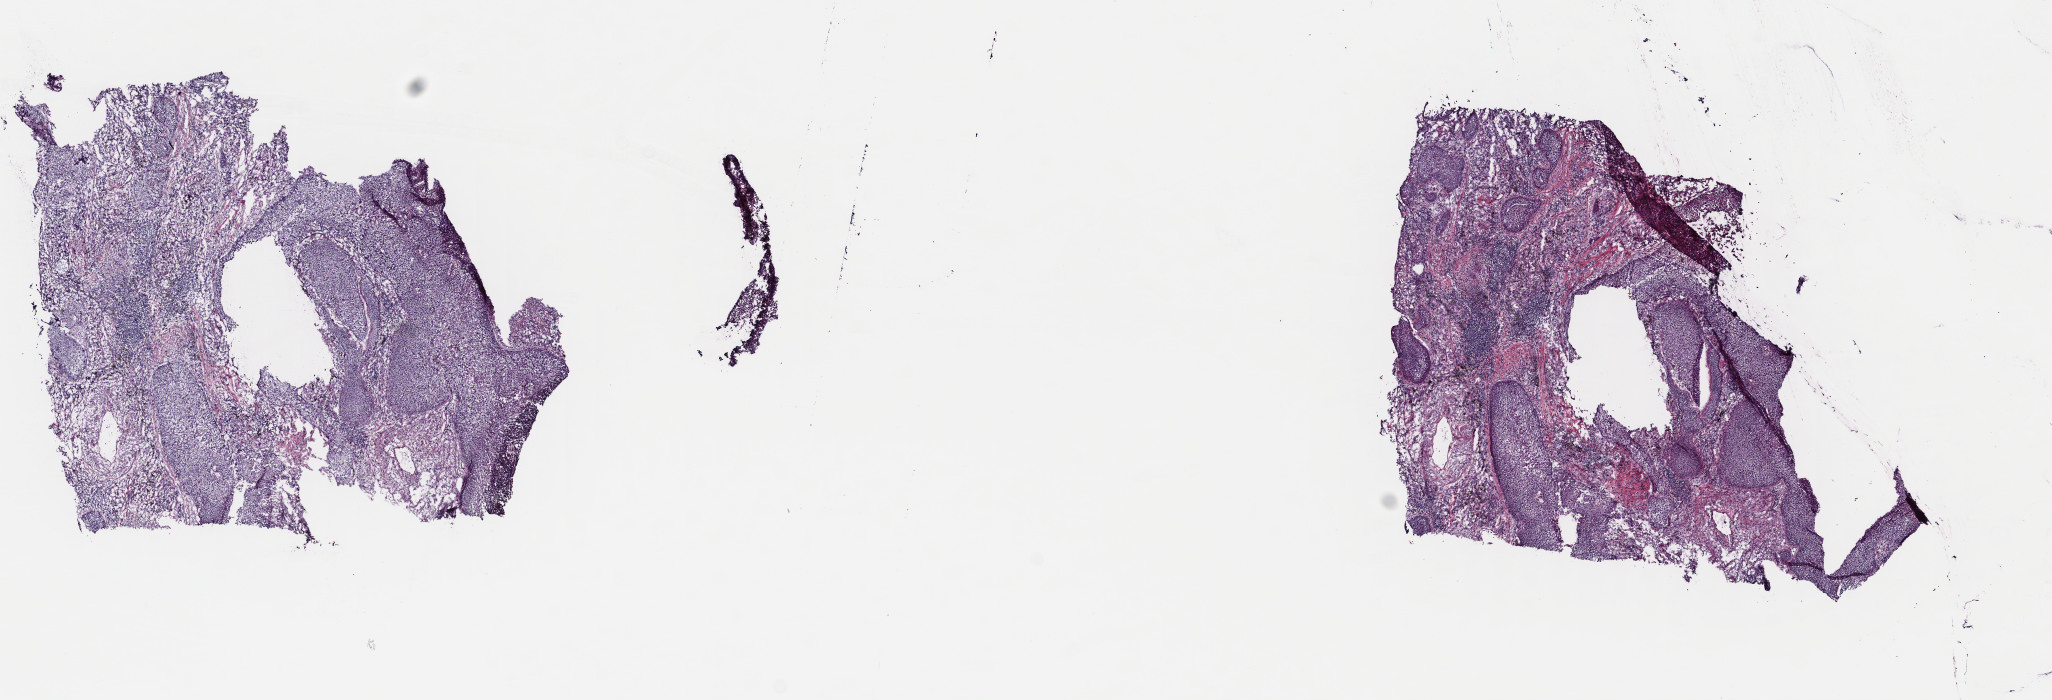
H&E whole-slide image, a low-resolution overview of the entire scanned area, about 16.2 x 5.5 mm (from a 40x scan), frozen section, lung, primary tumour sample. Female, age 72 years at initial diagnosis. Pathologist review of this section (percent, as recorded): tumour cells 70%, tumour nuclei 70%, normal cells 5%, stromal cells 20%, necrosis 5%. Infiltration values recorded for this section: lymphocyte infiltration 0%, monocyte infiltration 0%, neutrophil infiltration 0%.
• diagnosis: Squamous cell carcinoma, NOS (lower lobe, lung)
• AJCC pathologic stage: IB
• laterality: right